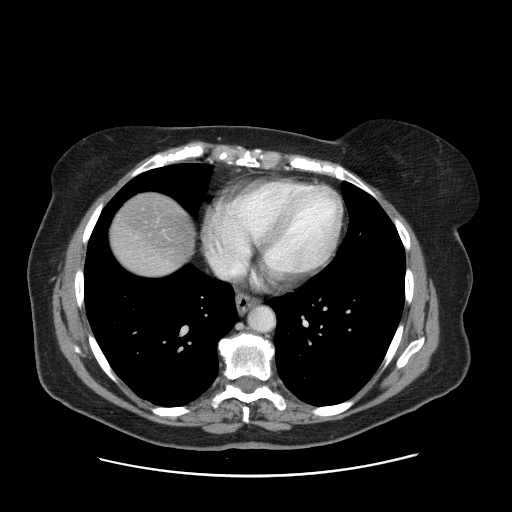
Contrast-enhanced abdominal CT, one axial slice. Position 149 of 161 along the scan axis. Intravenous contrast given. Soft-tissue window (W 400 / L 40 HU). 512 × 512 image matrix. Female patient, age 62 years. From the clinical record (not read from this slice): diagnosis: colorectal cancer liver metastases, imaged before liver resection; multiple liver metastases: no; largest metastasis: 2.5 cm.
Outlined on this slice (manually delineated by an expert):
- liver: bounding box (x1, y1, x2, y2) in pixels: (112, 194, 193, 274)
- planned liver remnant (the part of the liver to remain after resection): (112, 194, 193, 268)